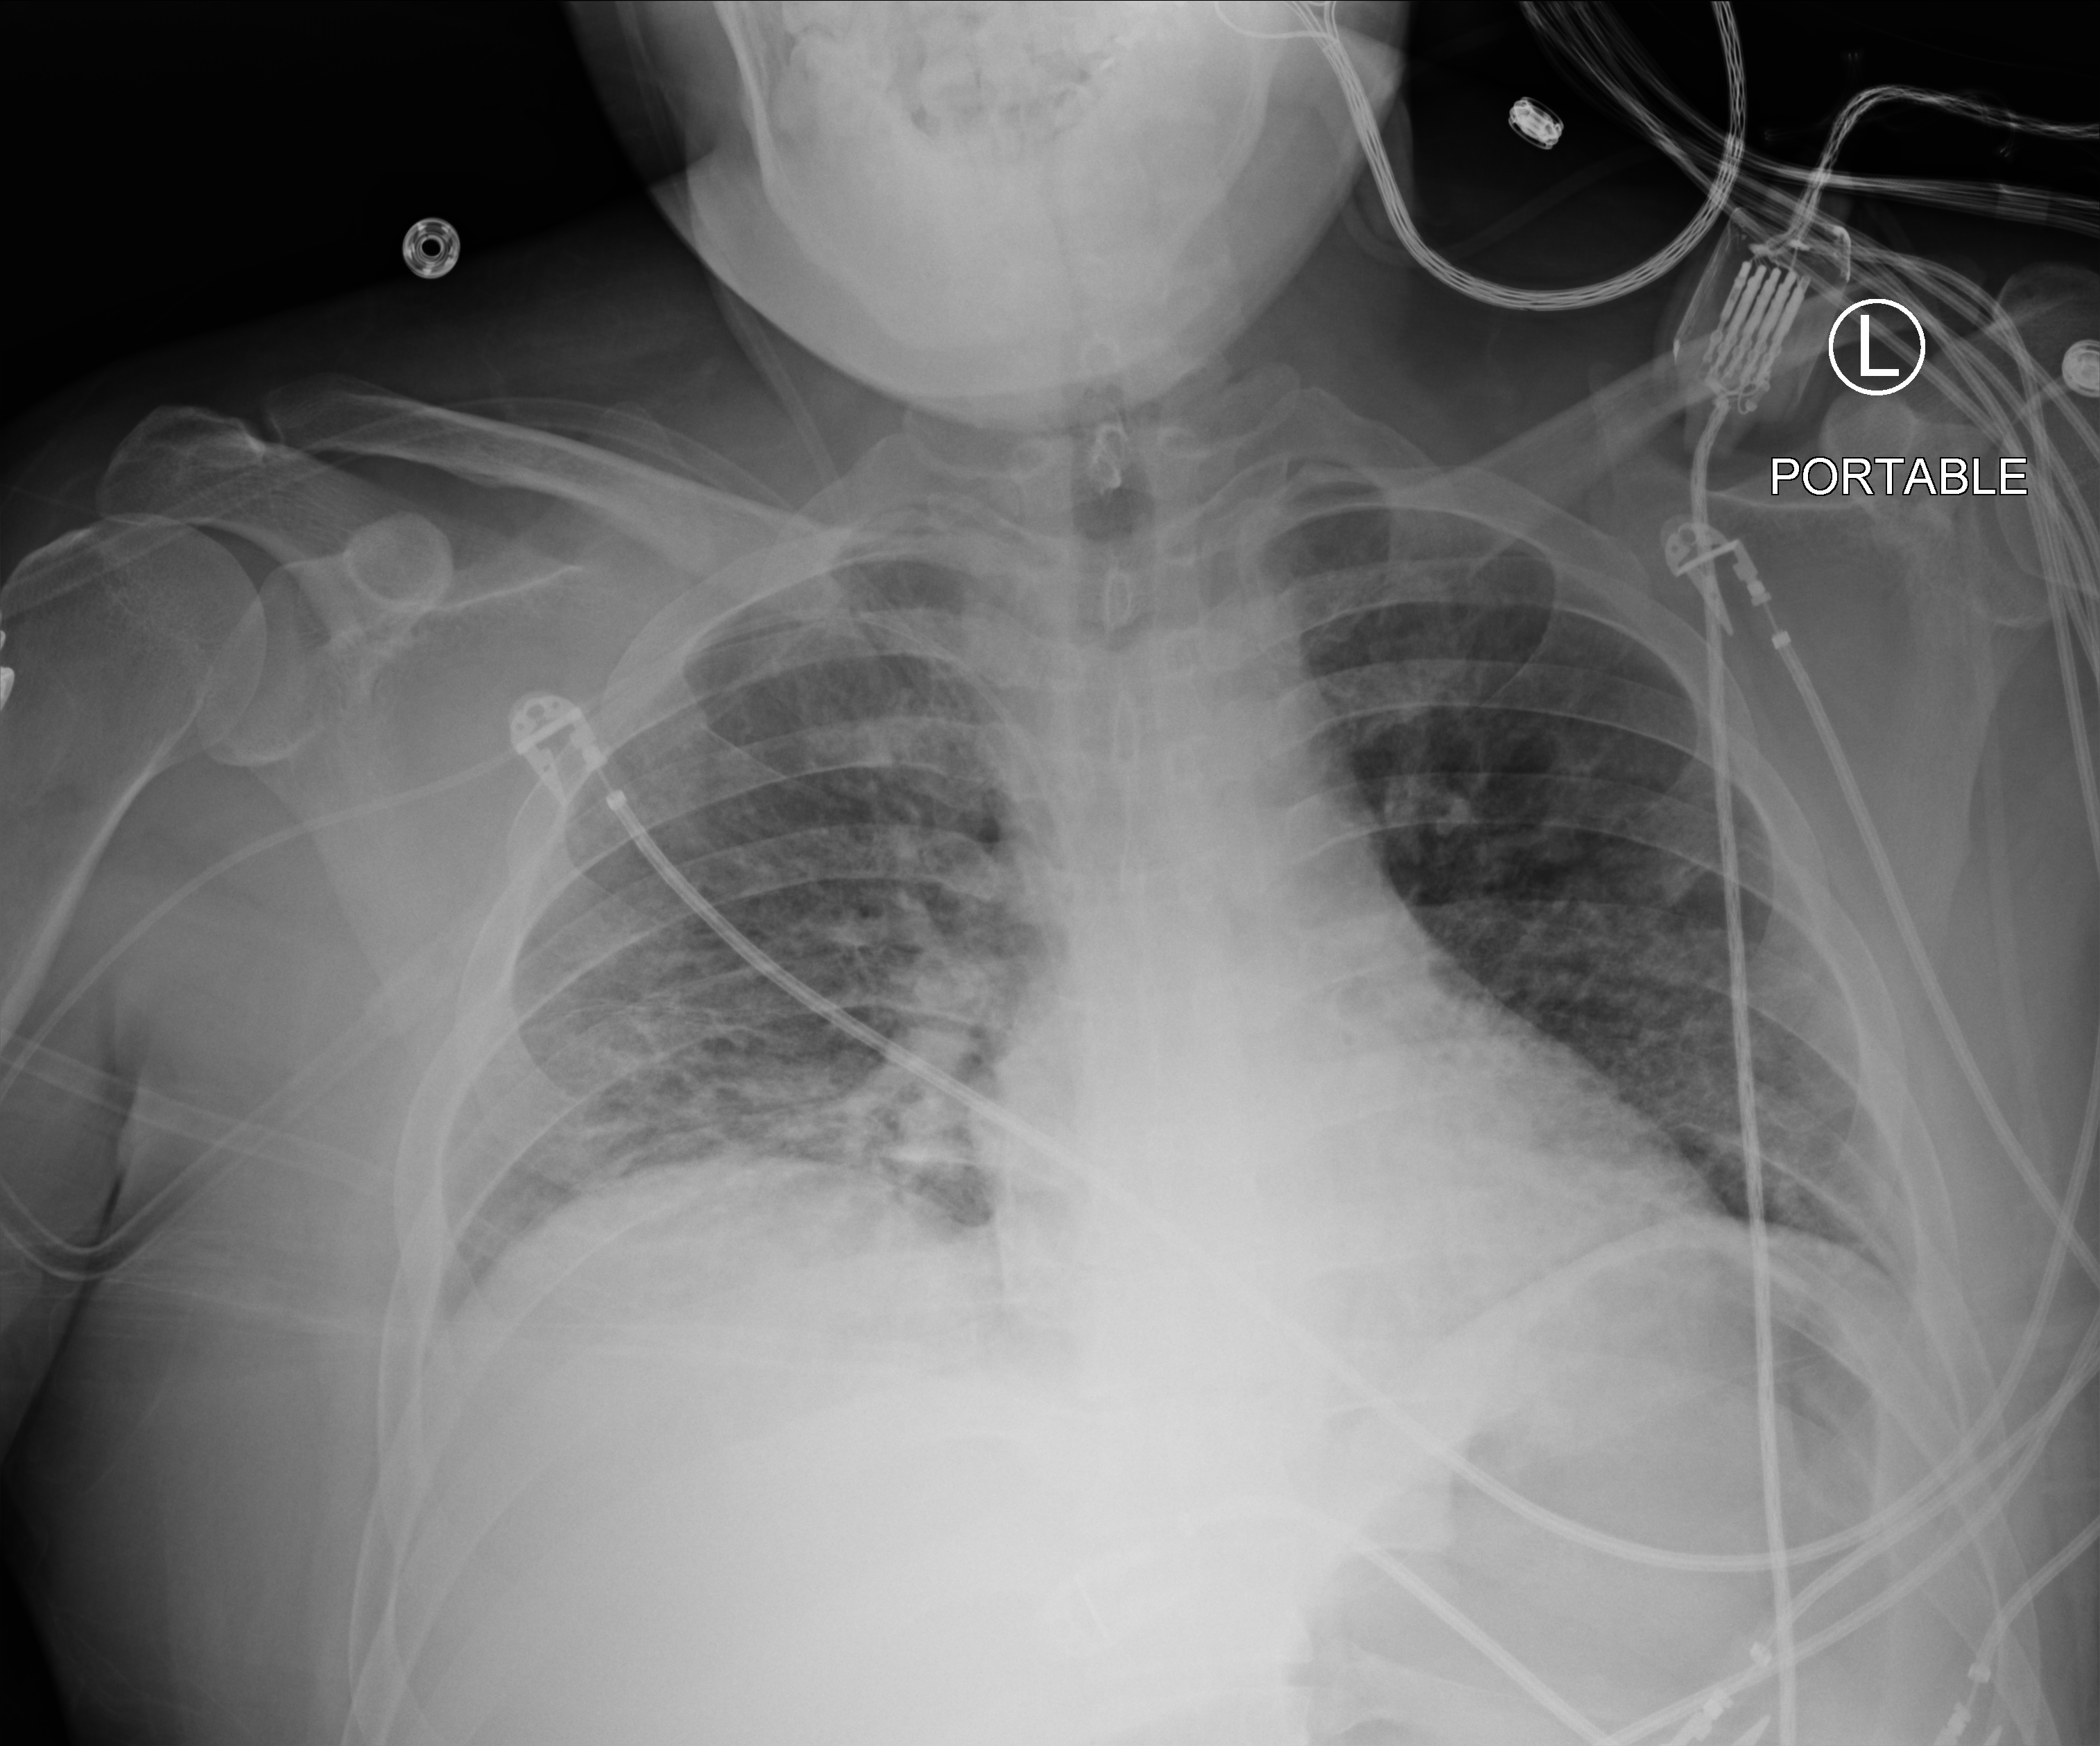
Portable chest radiograph; anteroposterior (AP) projection. Male patient hospitalised with COVID-19, age 18–59 years.
Hospital-stay facts (about this admission, not read from this image; timing relative to this image not recorded): mechanically ventilated during this hospital stay: yes.